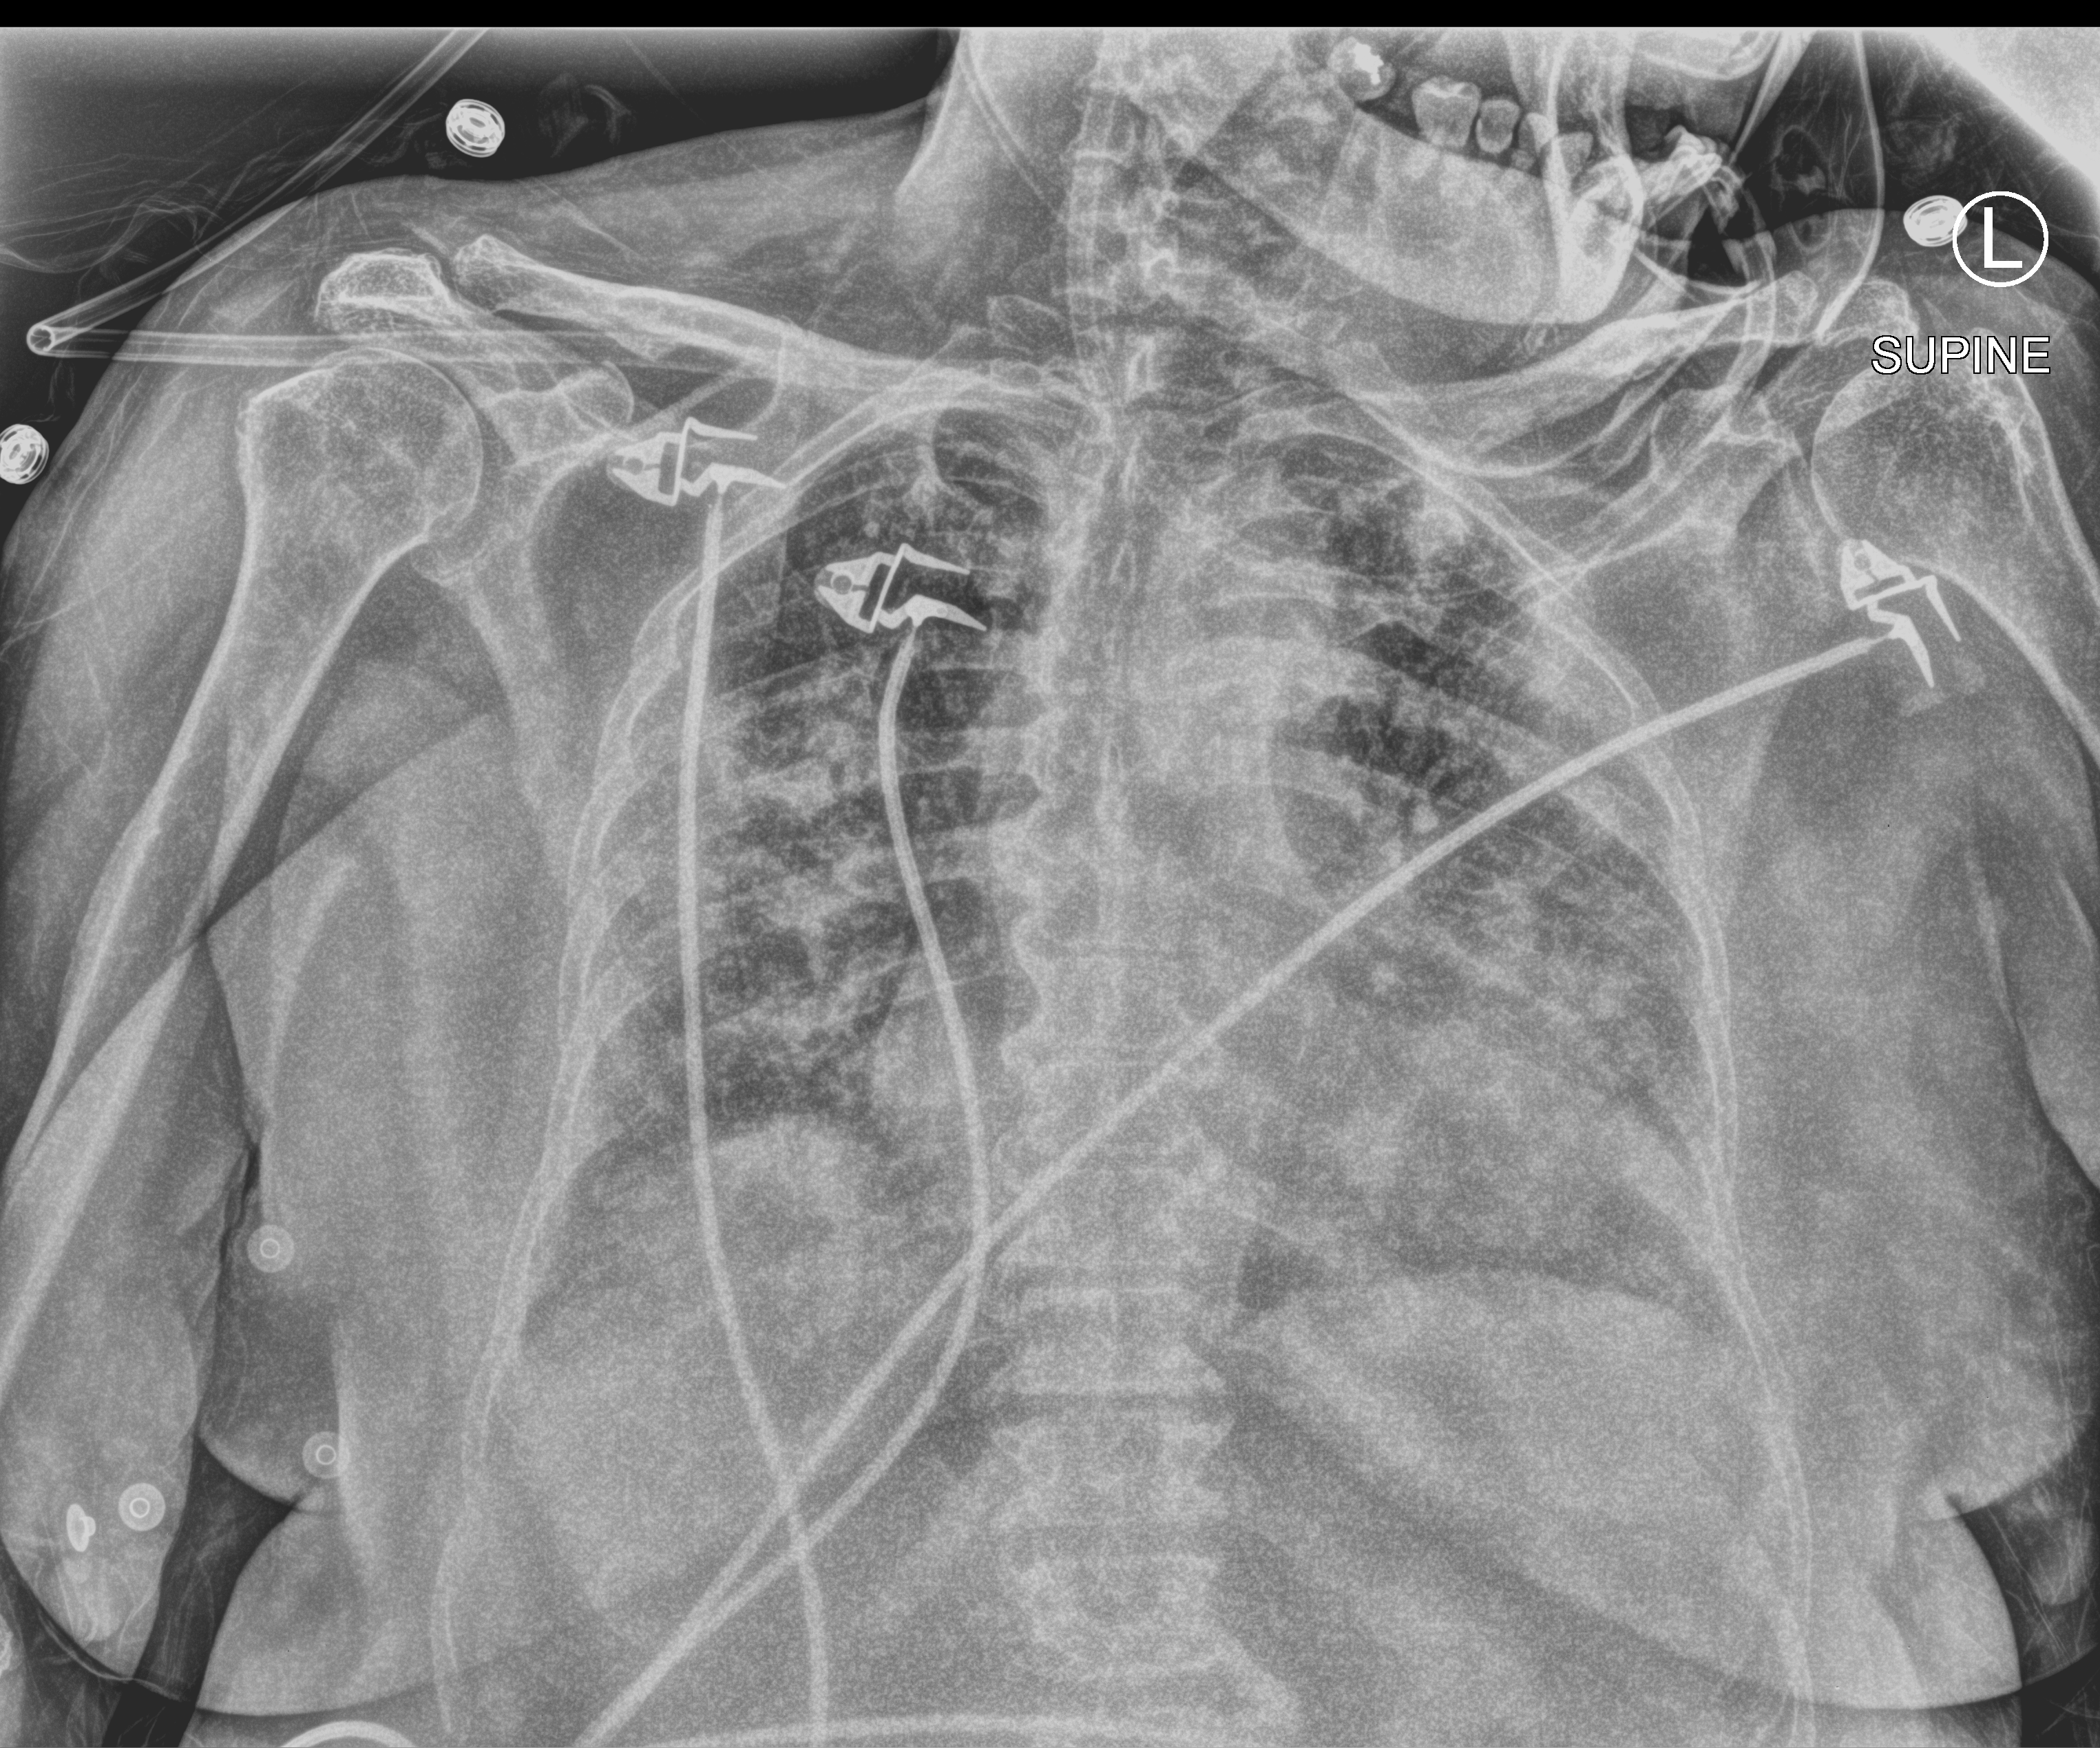
Bedside chest radiograph (computed radiography). Patient hospitalised with COVID-19; female, aged 75–90 years.
Admission-level facts for this patient (not findings on this image; timing relative to this image not recorded): admitted to intensive care during this hospital stay: yes.